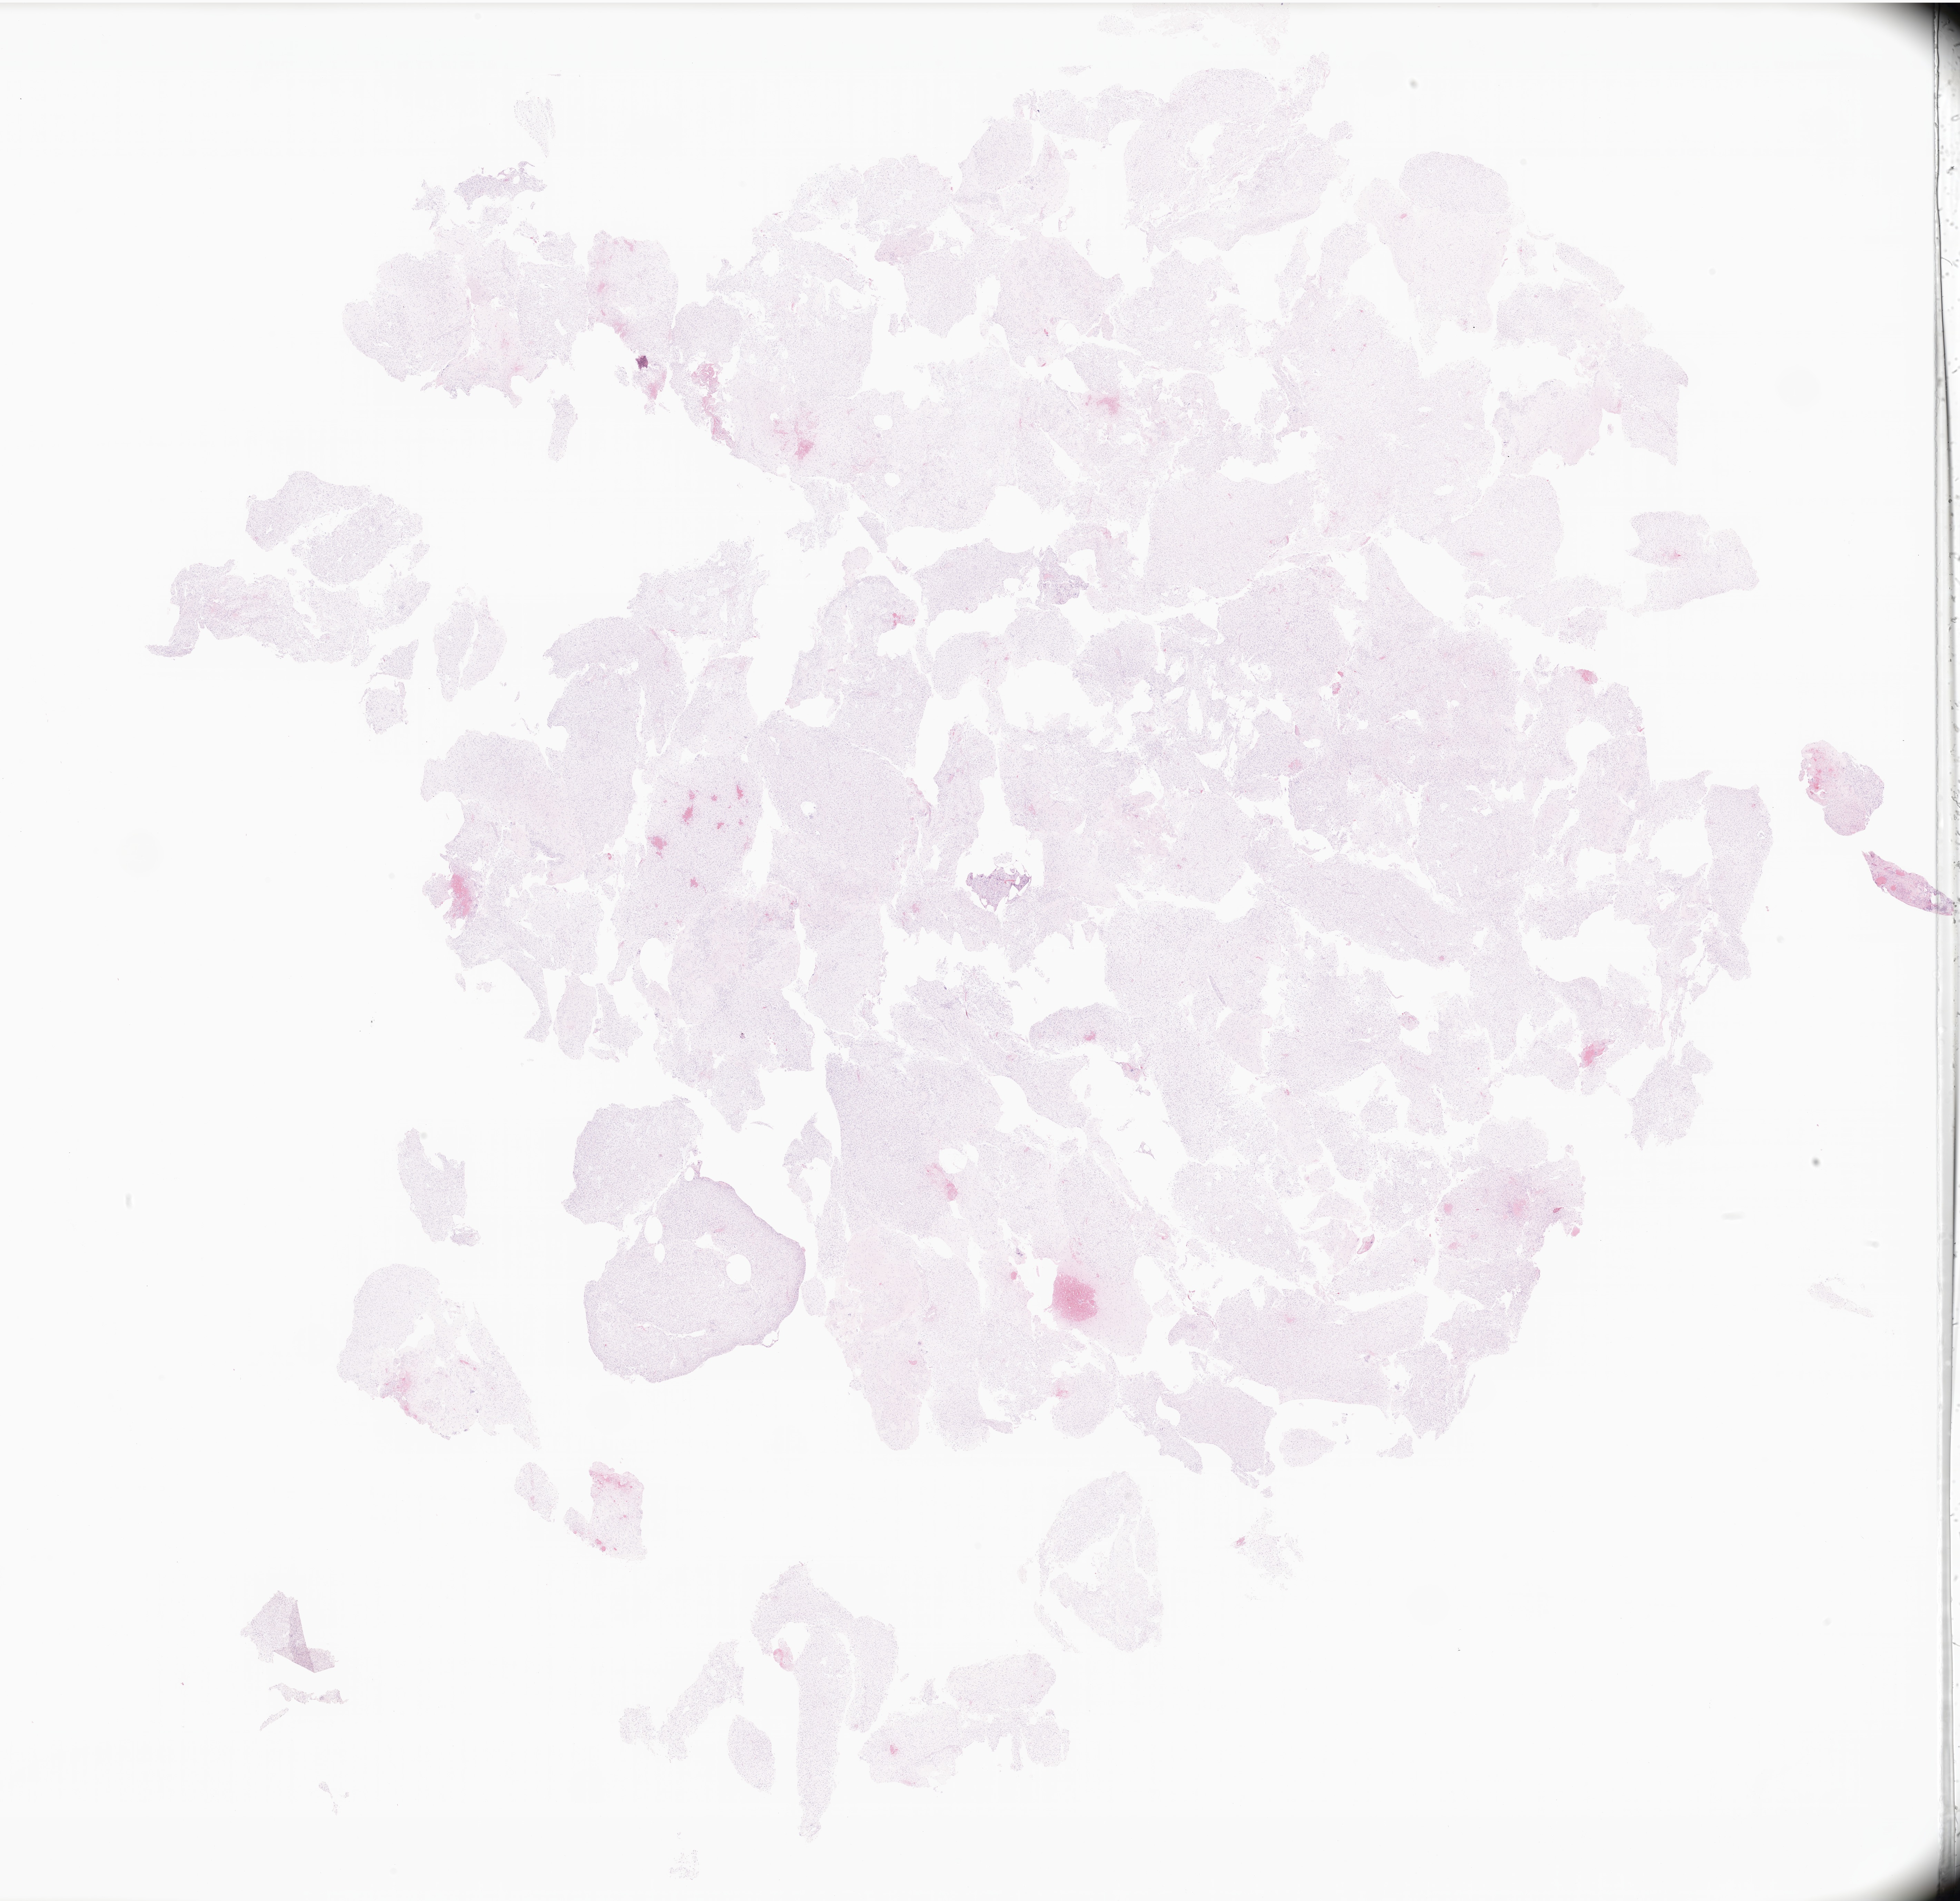
Whole-slide image, hematoxylin and eosin (H&E) stain of tumor tissue from the brain, low-resolution overview of the scanned area, about 24.0 x 23.2 mm; FFPE section. Female patient, age 199 months (16 years 7 months).
Diagnosis: Pilocytic astrocytoma.